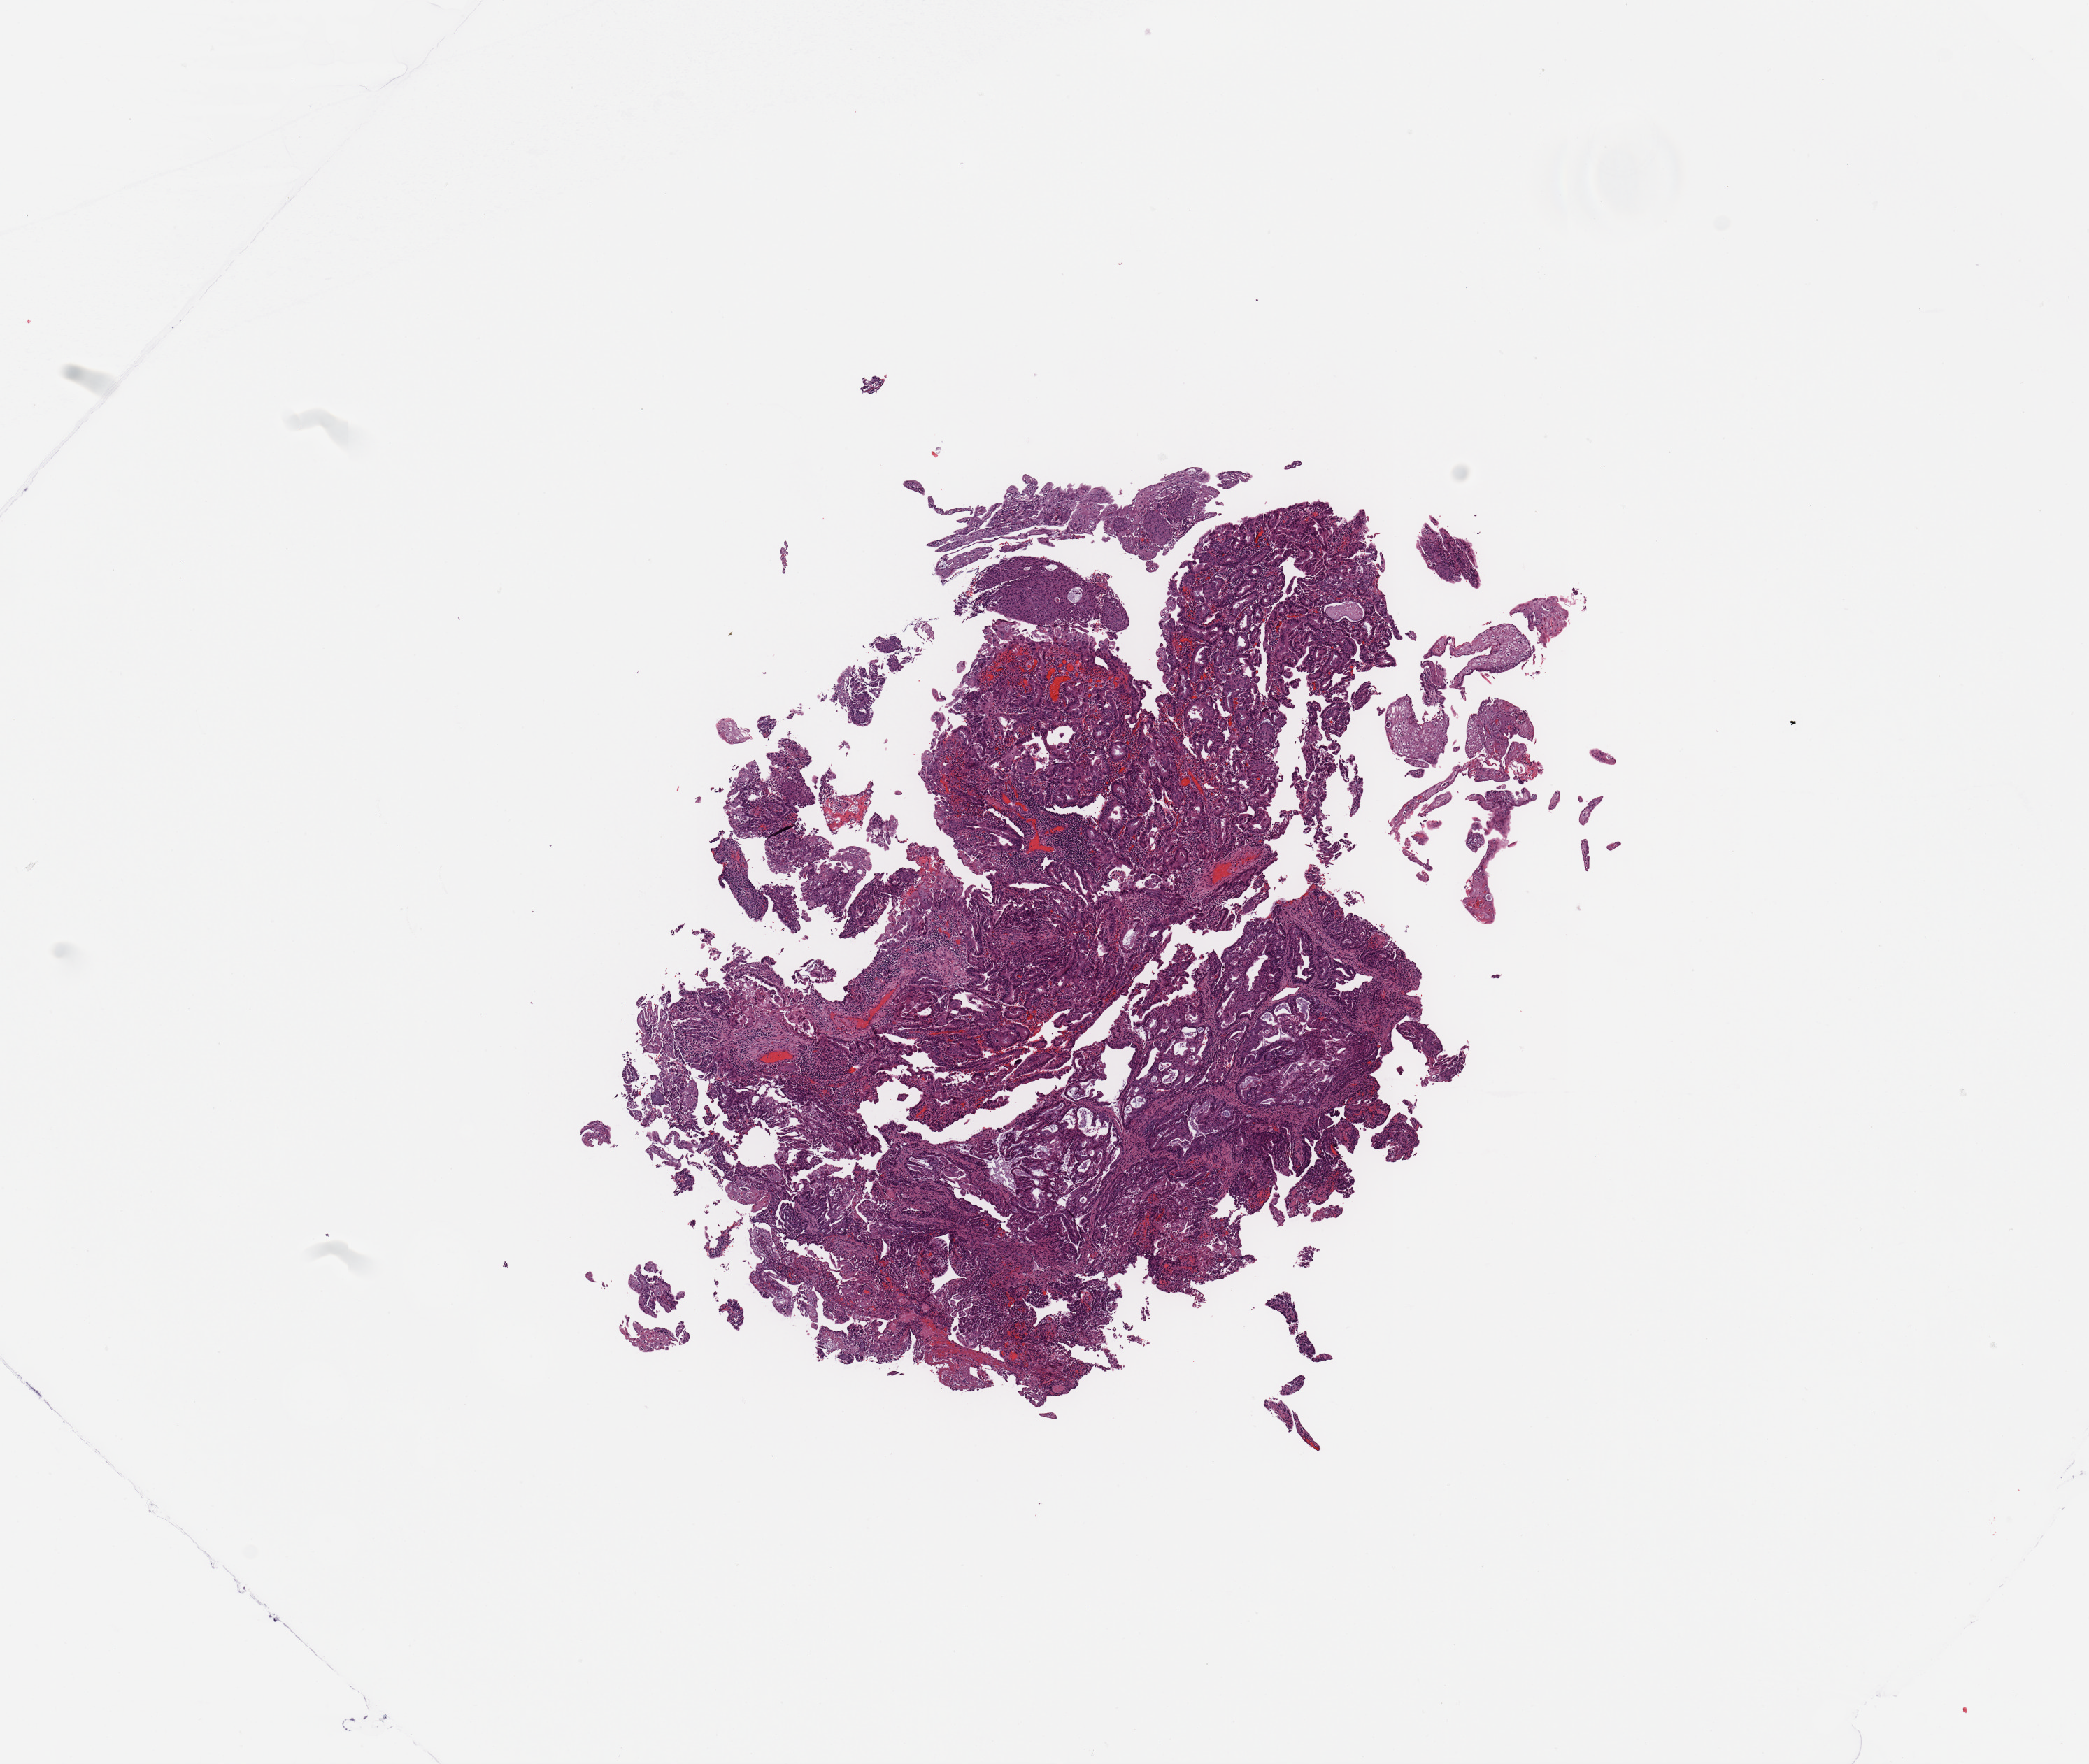
Digitized Hematoxylin and eosin (H&E) stained tissue section (whole slide) — a low-resolution overview of the entire scanned area, about 11.8 x 10.0 mm (acquisition: 20x scan), uterus, tumour tissue. Female, 54 y/o.
Diagnosis: Endometrioid adenocarcinoma, NOS.